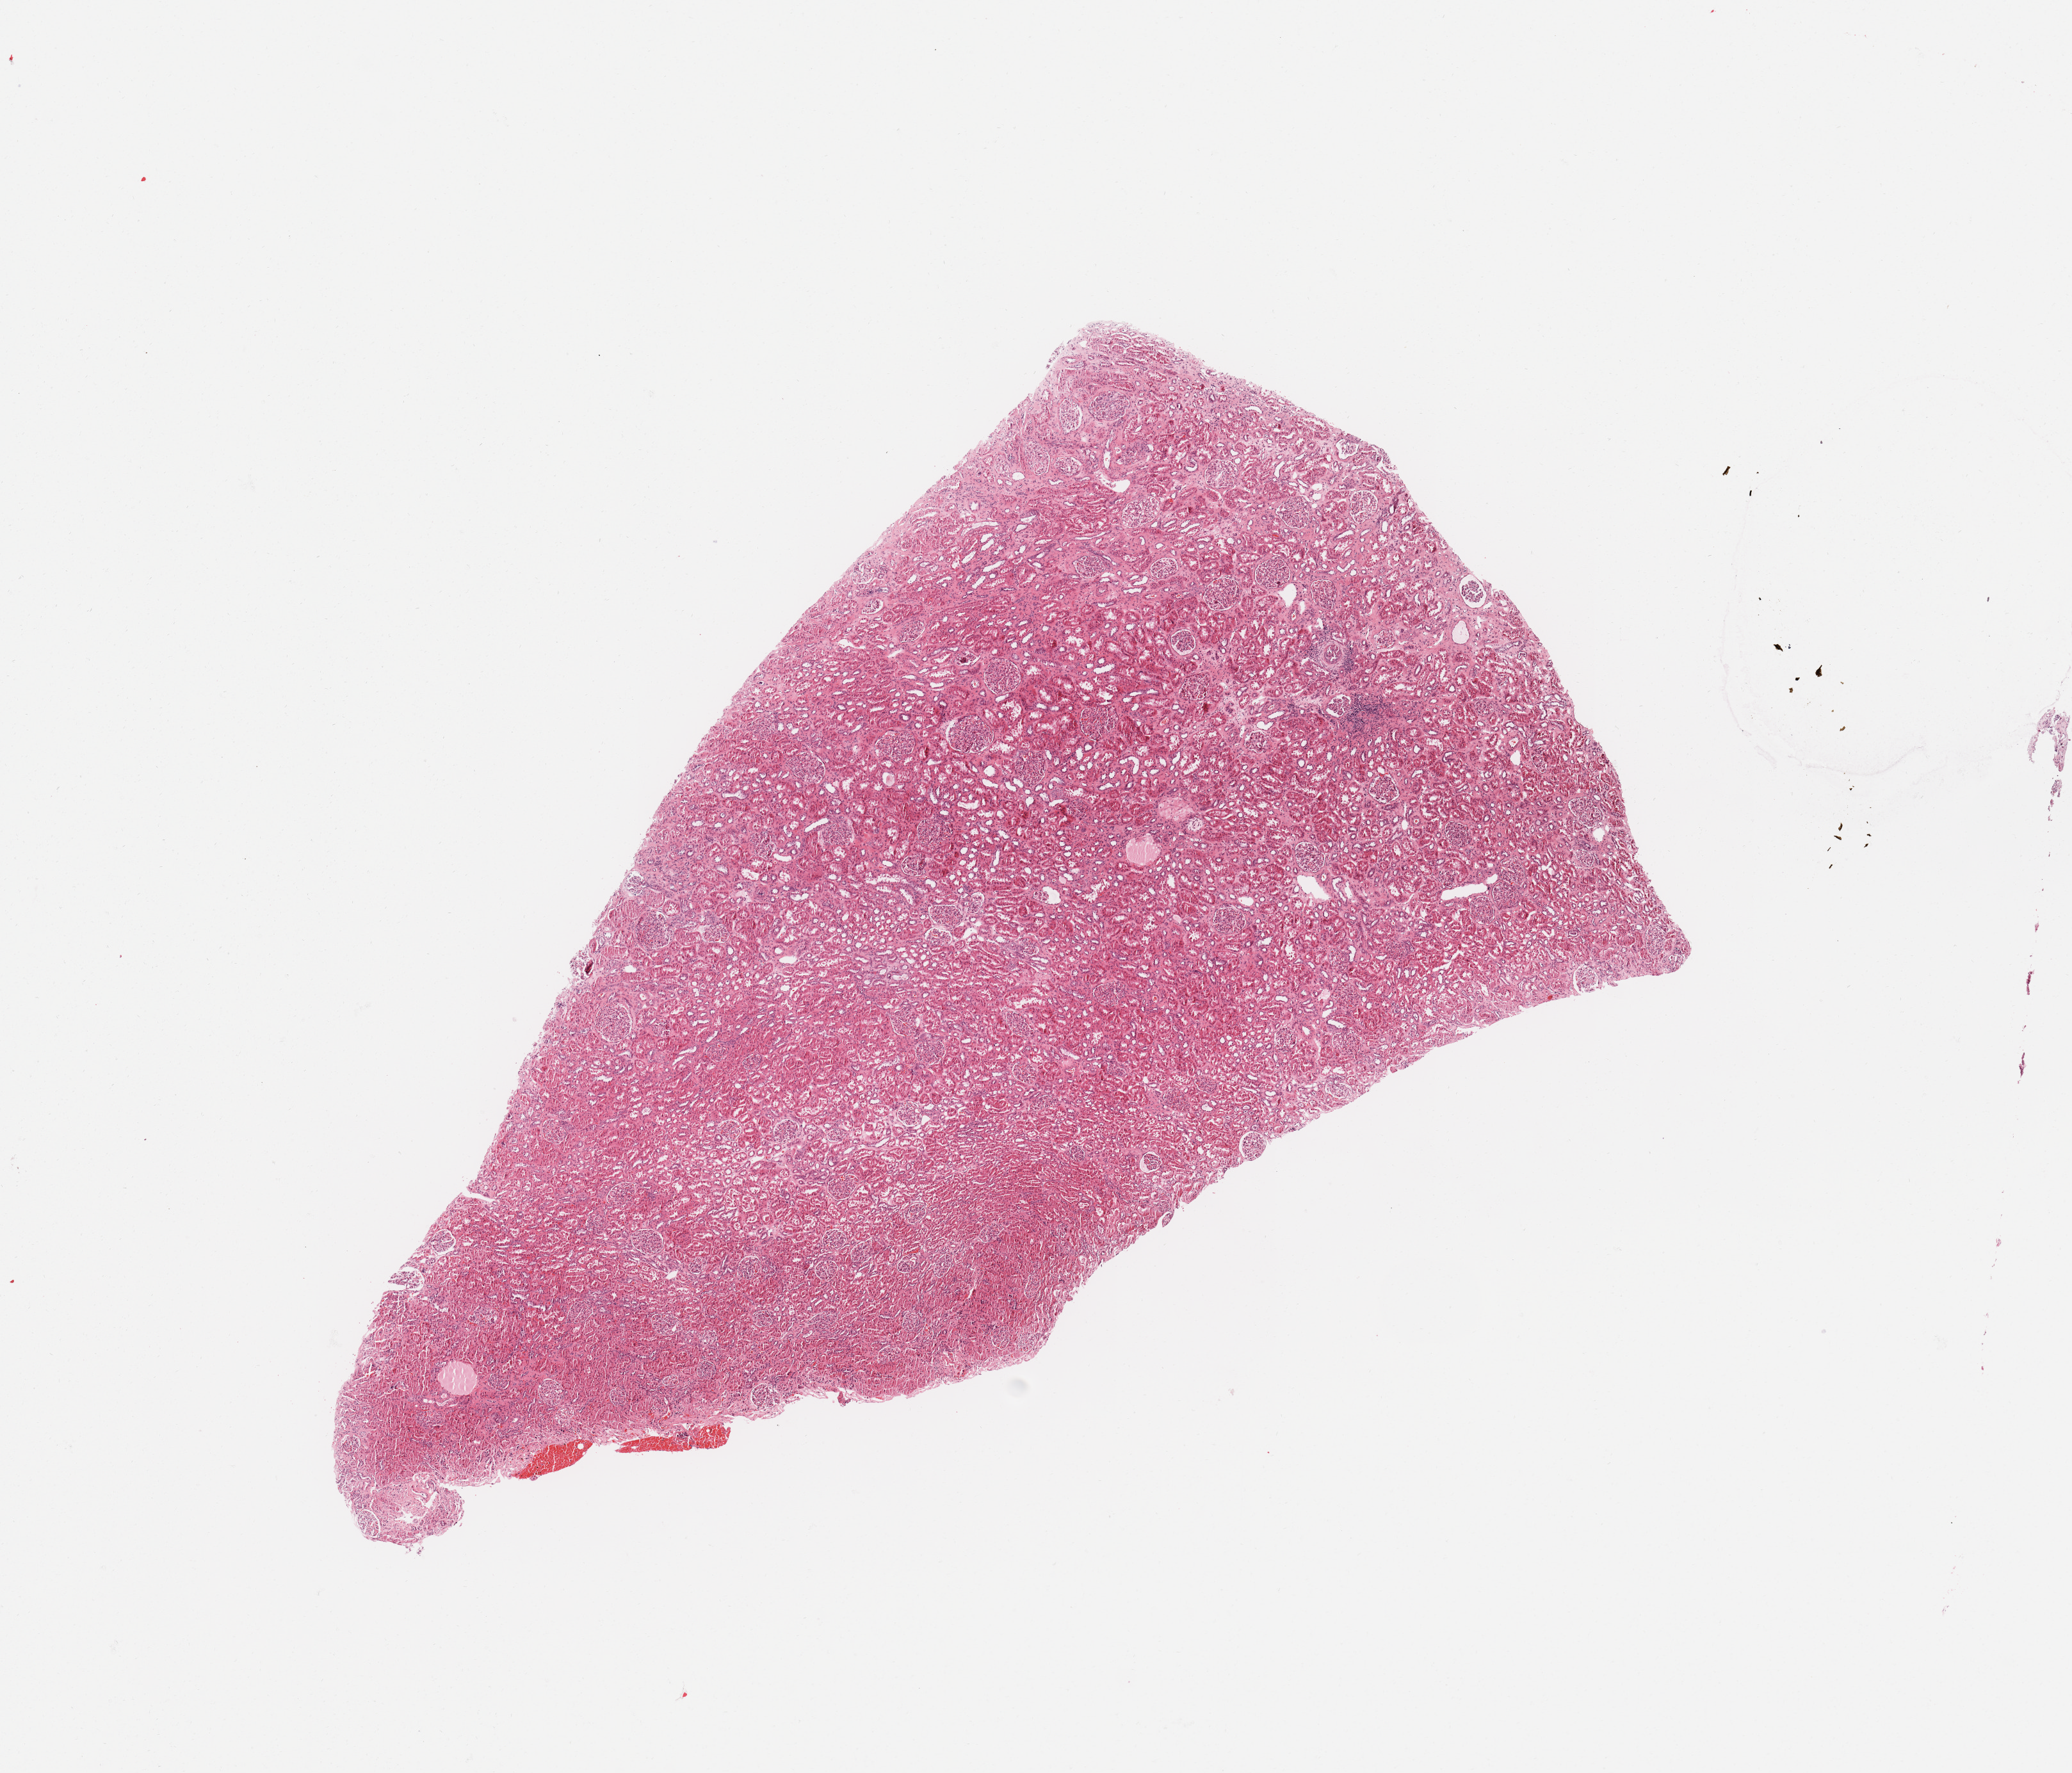
Digitized H&E tissue section (whole slide) — shown as a low-resolution overview of the whole scanned area (about 12.8 x 11.0 mm, acquisition: 20x scan); kidney, normal (non-tumour) tissue. Male, 31 y/o.
- this section: normal (non-tumour) tissue from the same patient
- patient diagnosis: Renal cell carcinoma, NOS